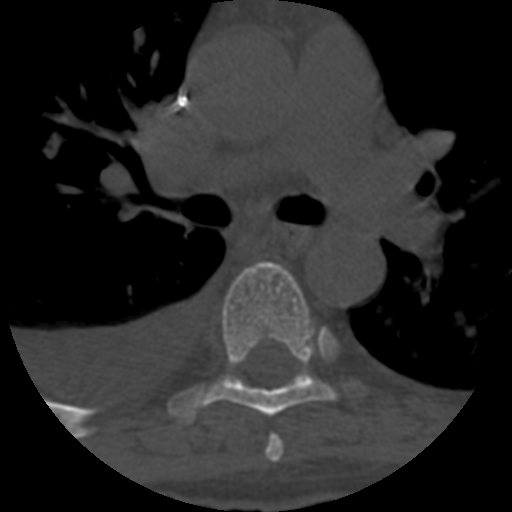
CT including the spine, one axial slice; slice 436 of 708 in the series (ordered by position); one of 3 acquisitions stored at this slice position; bone window (W 1800 / L 400 HU); 1.25 mm slice thickness; 512 × 512 image matrix. Patient age 55 years. Case-level facts recorded for this patient, not image findings: primary cancer: colon; vertebrae with lytic lesions (as recorded): T12, L1, L5.
Annotated regions visible in this slice (semi-automatically segmented with operator editing):
- T5 vertebra: bounding box <265,436,283,462> (left, top, right, bottom; pixels)
- T6 vertebra: <176,262,360,425>